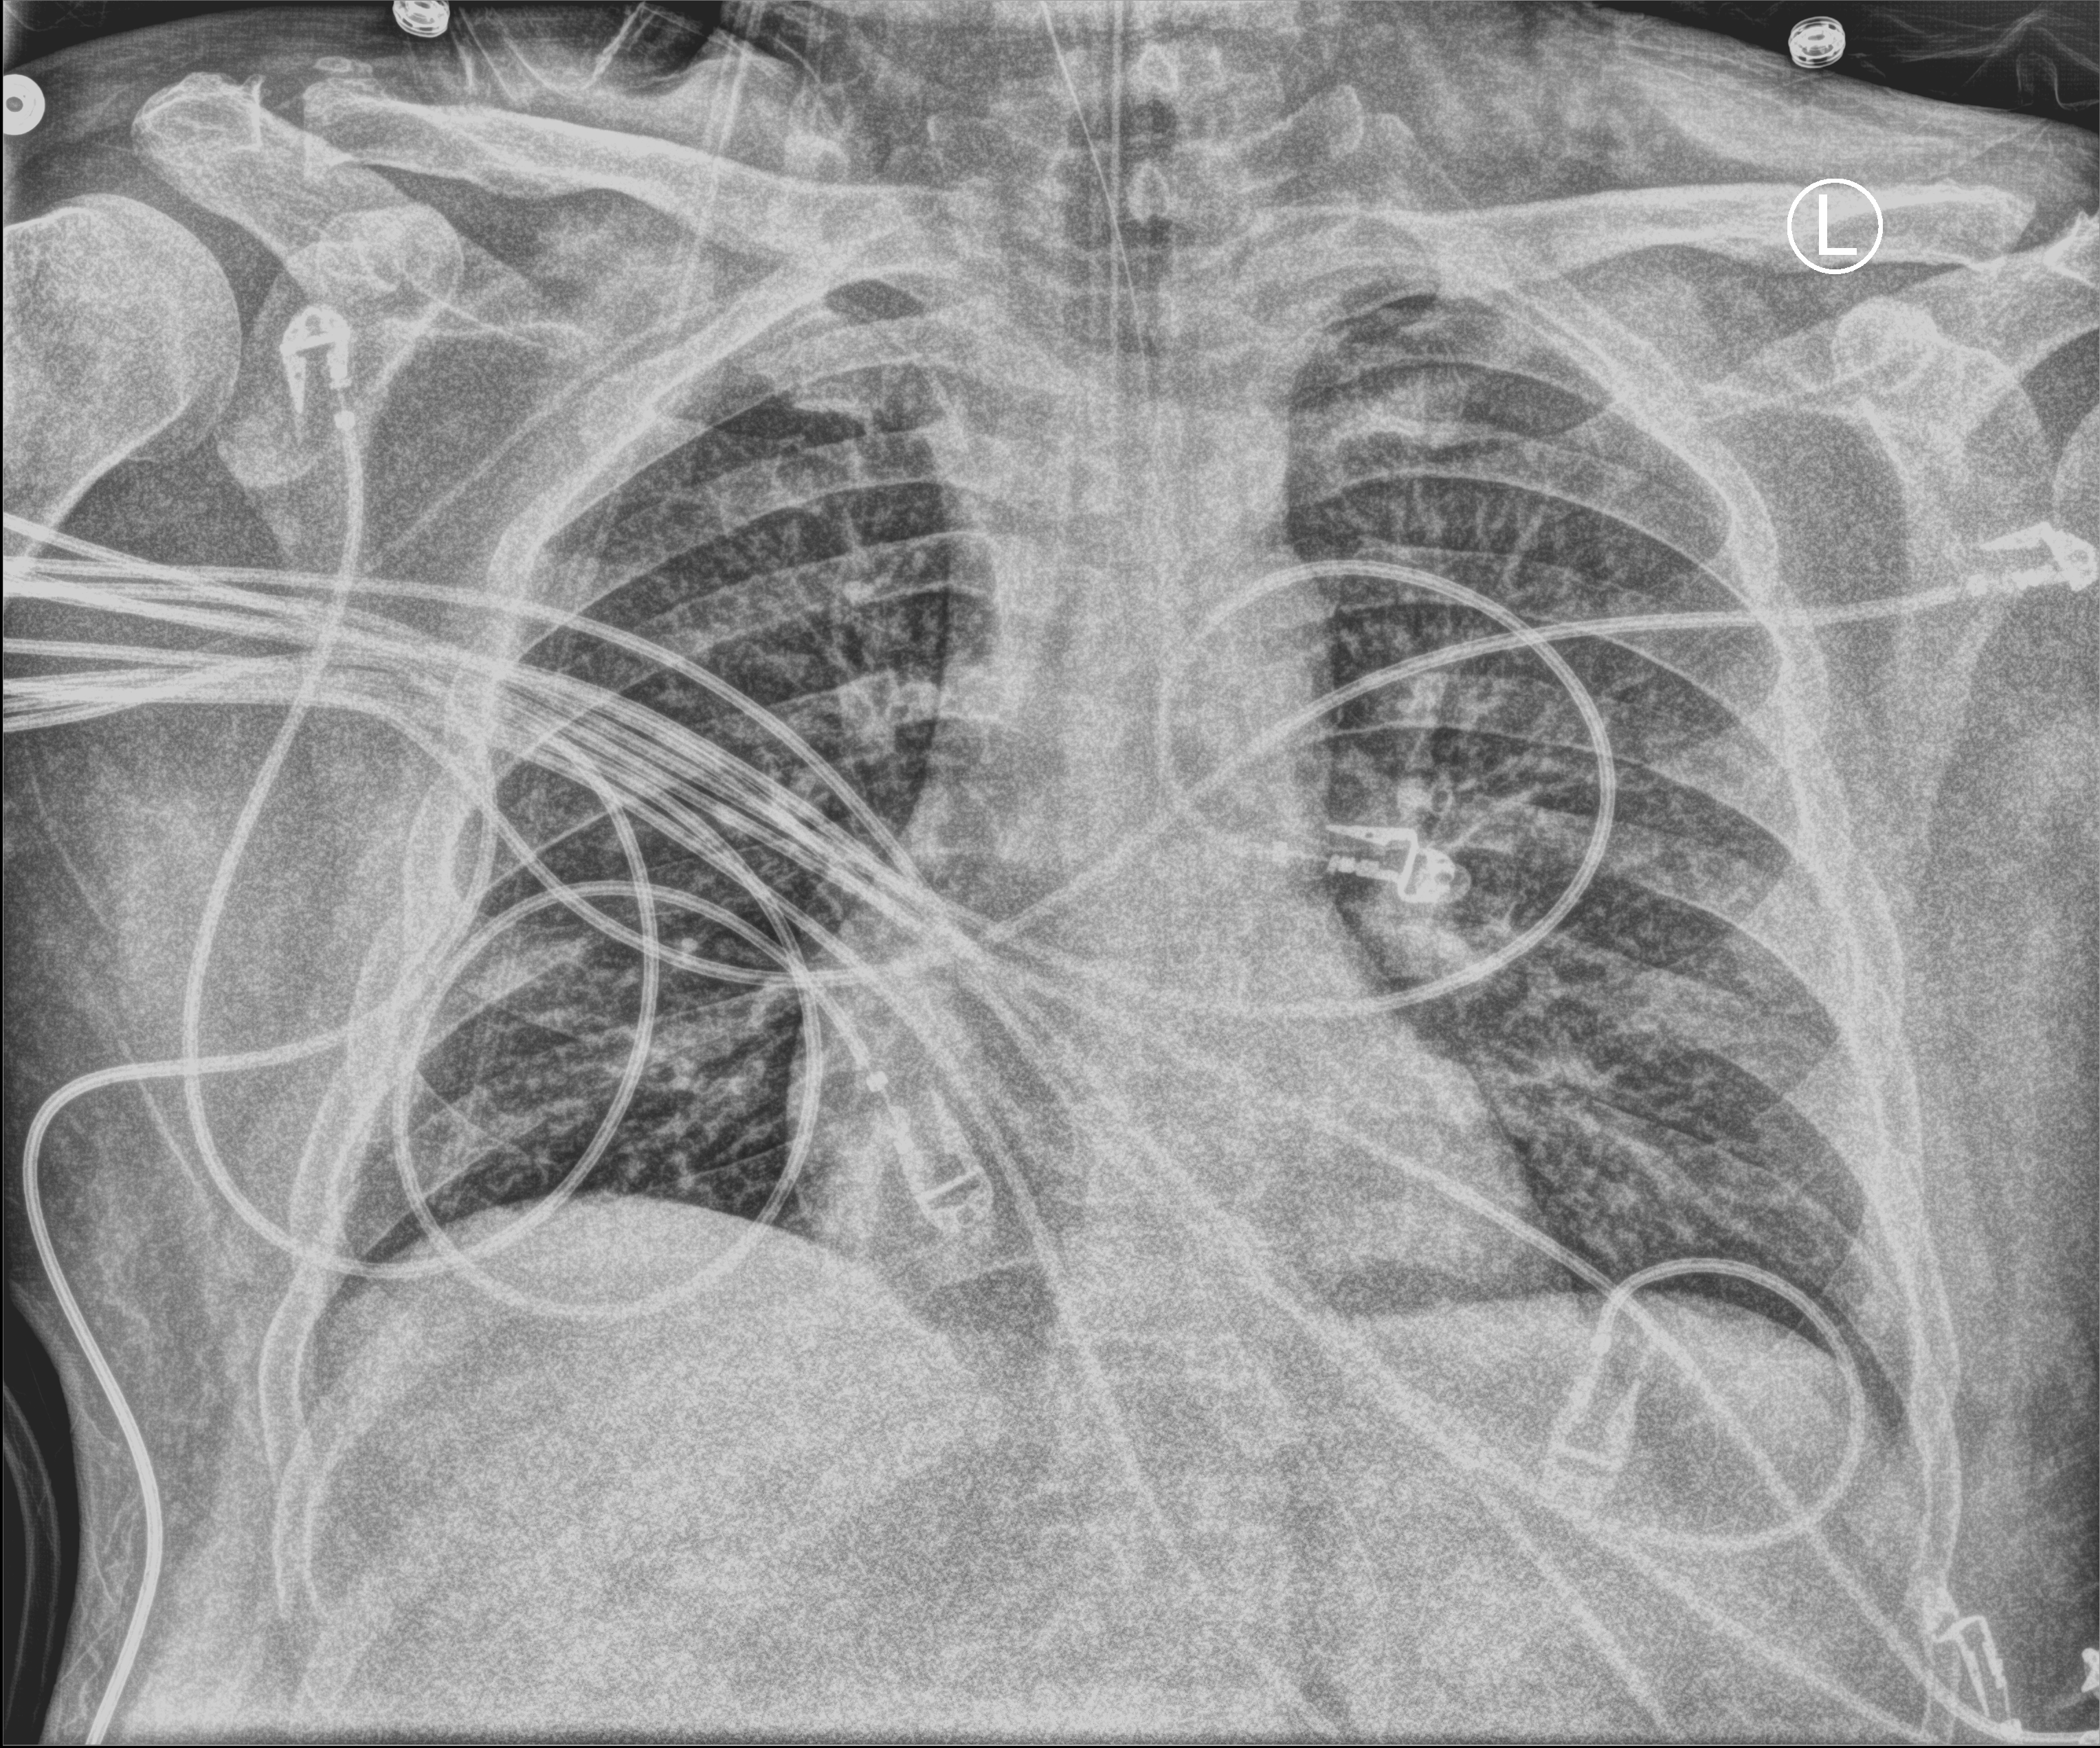
Chest X-ray (portable). Patient hospitalised with COVID-19; male, aged 18–59 years.
Hospital-stay facts (about this admission, not read from this image; timing relative to this image not recorded): admitted to intensive care during this hospital stay: yes; mechanically ventilated during this hospital stay: yes.